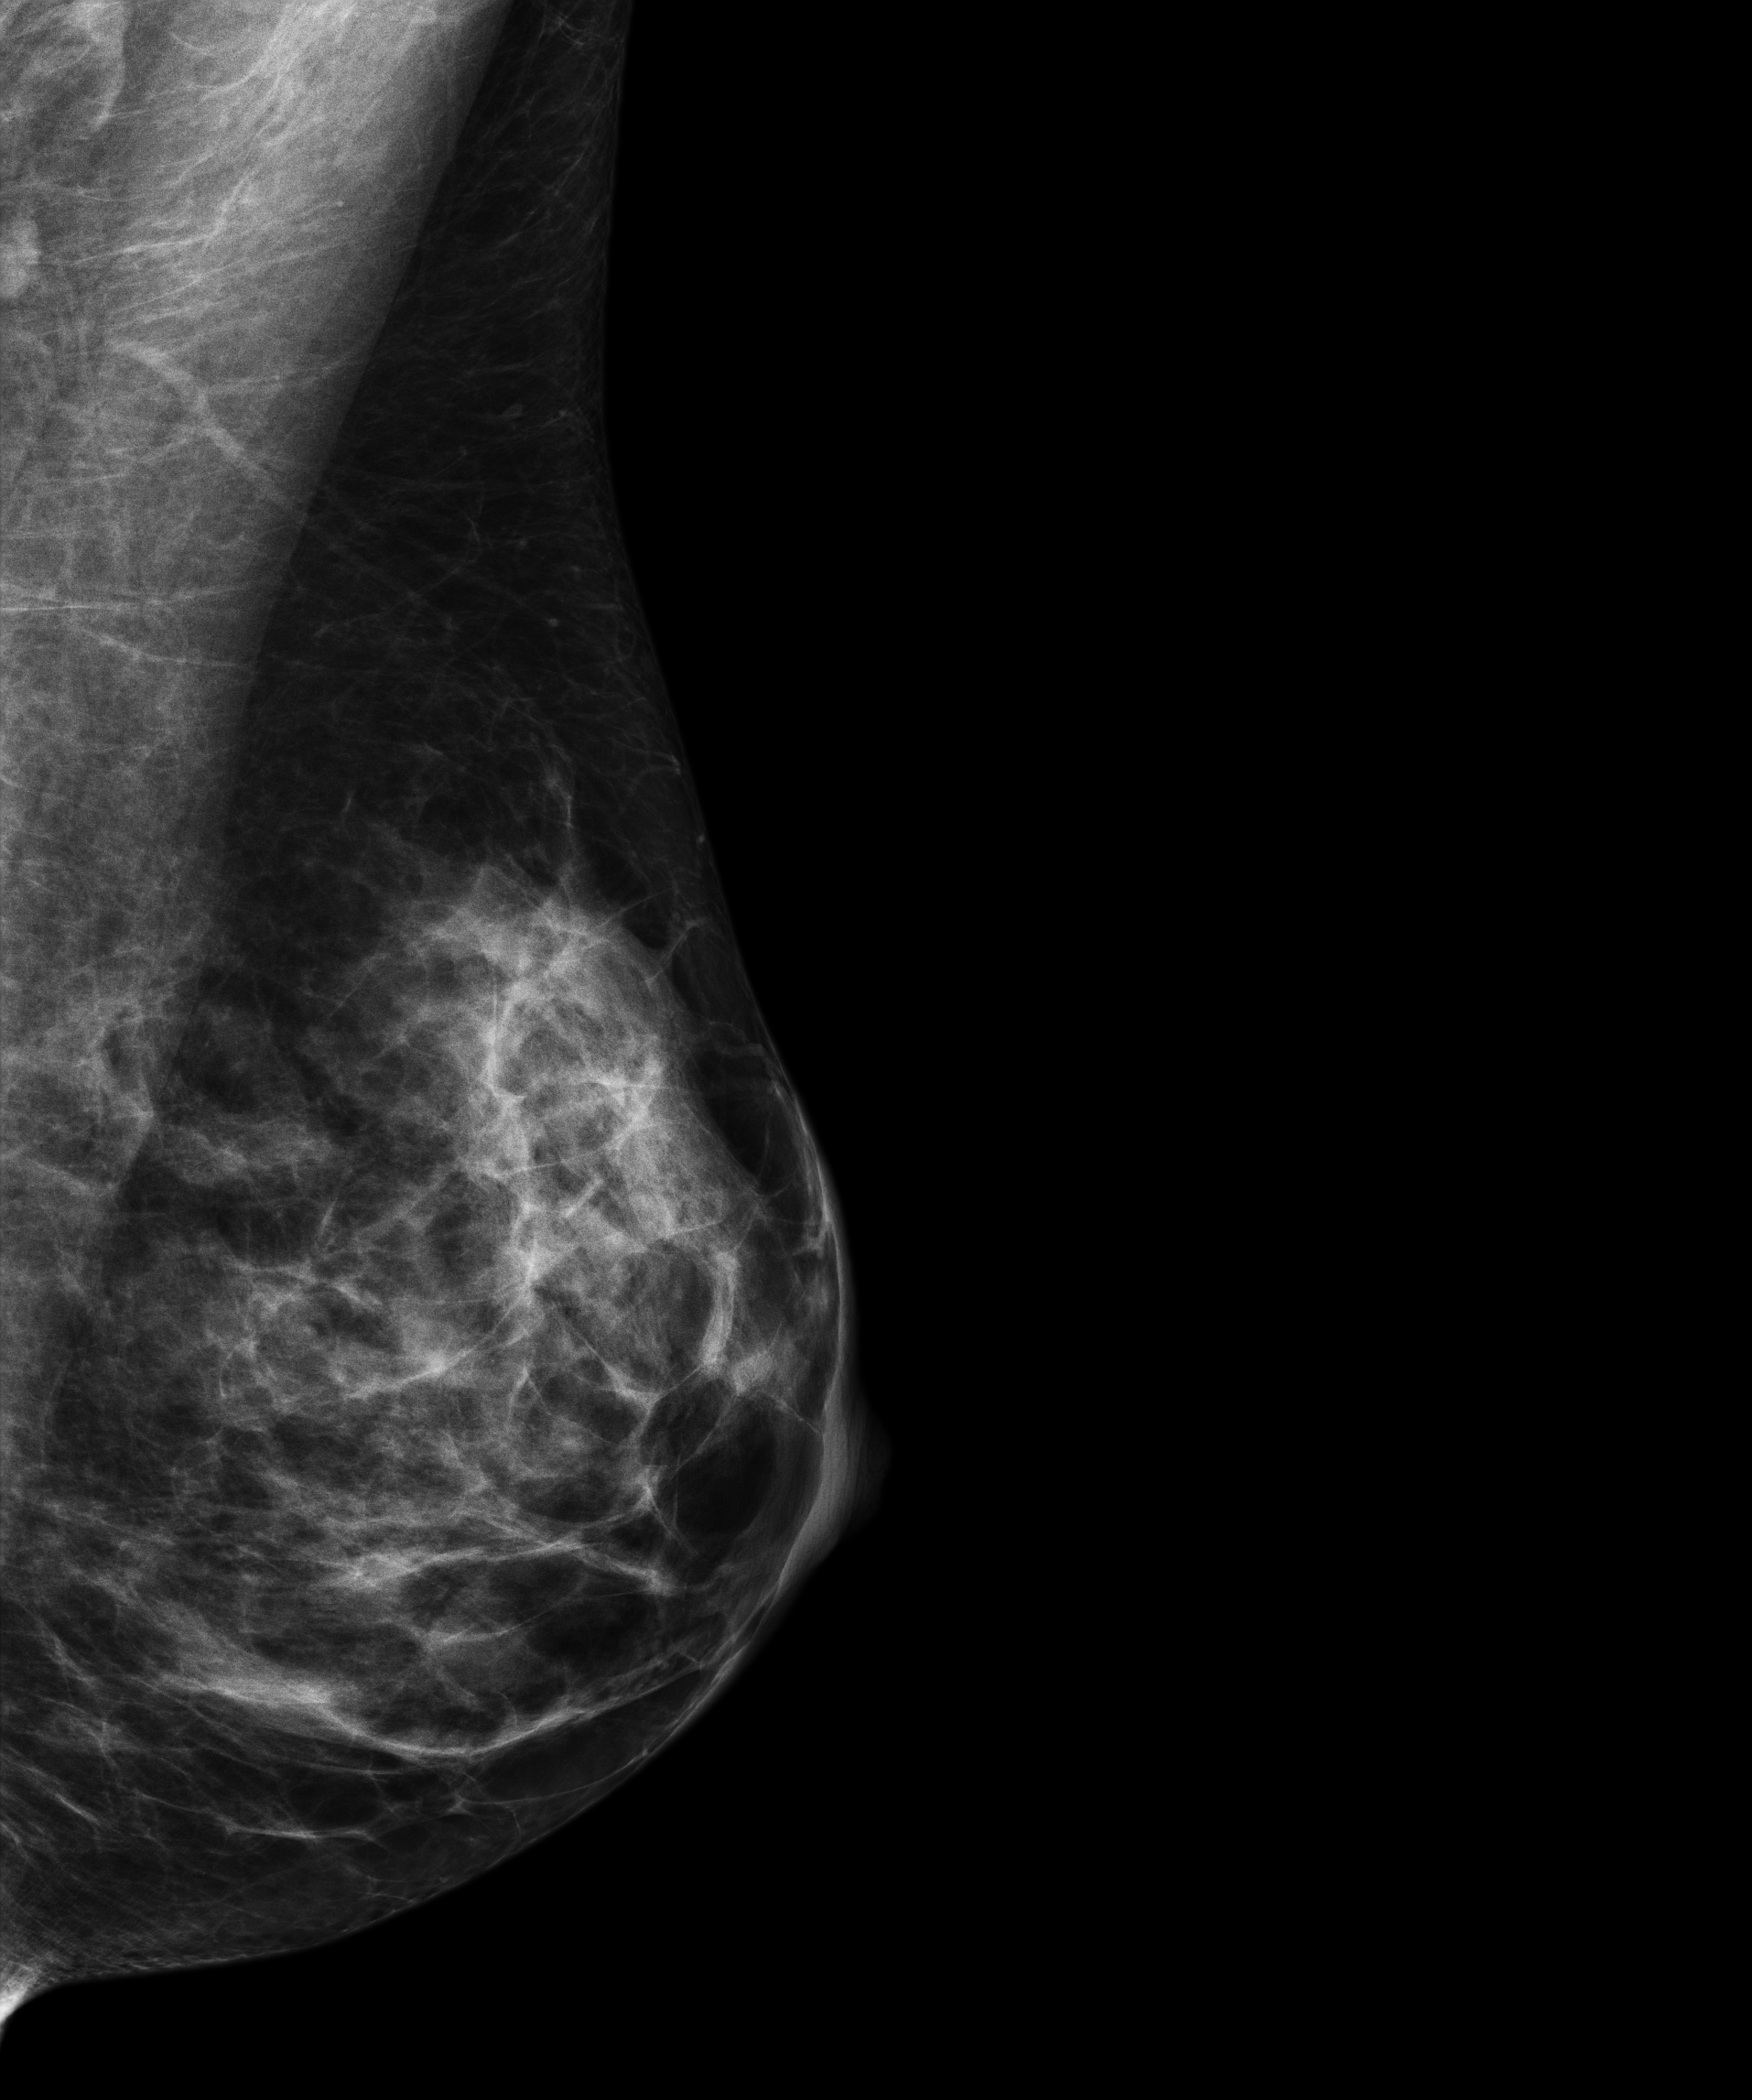
Annual screening mammography examination, compressed breast thickness 53 mm, system: Senographe Essential ADS_56.21.3. Female patient, age 45 years.
Image type: full-field digital mammogram. Breast: left. Projection: mediolateral oblique (MLO) view.